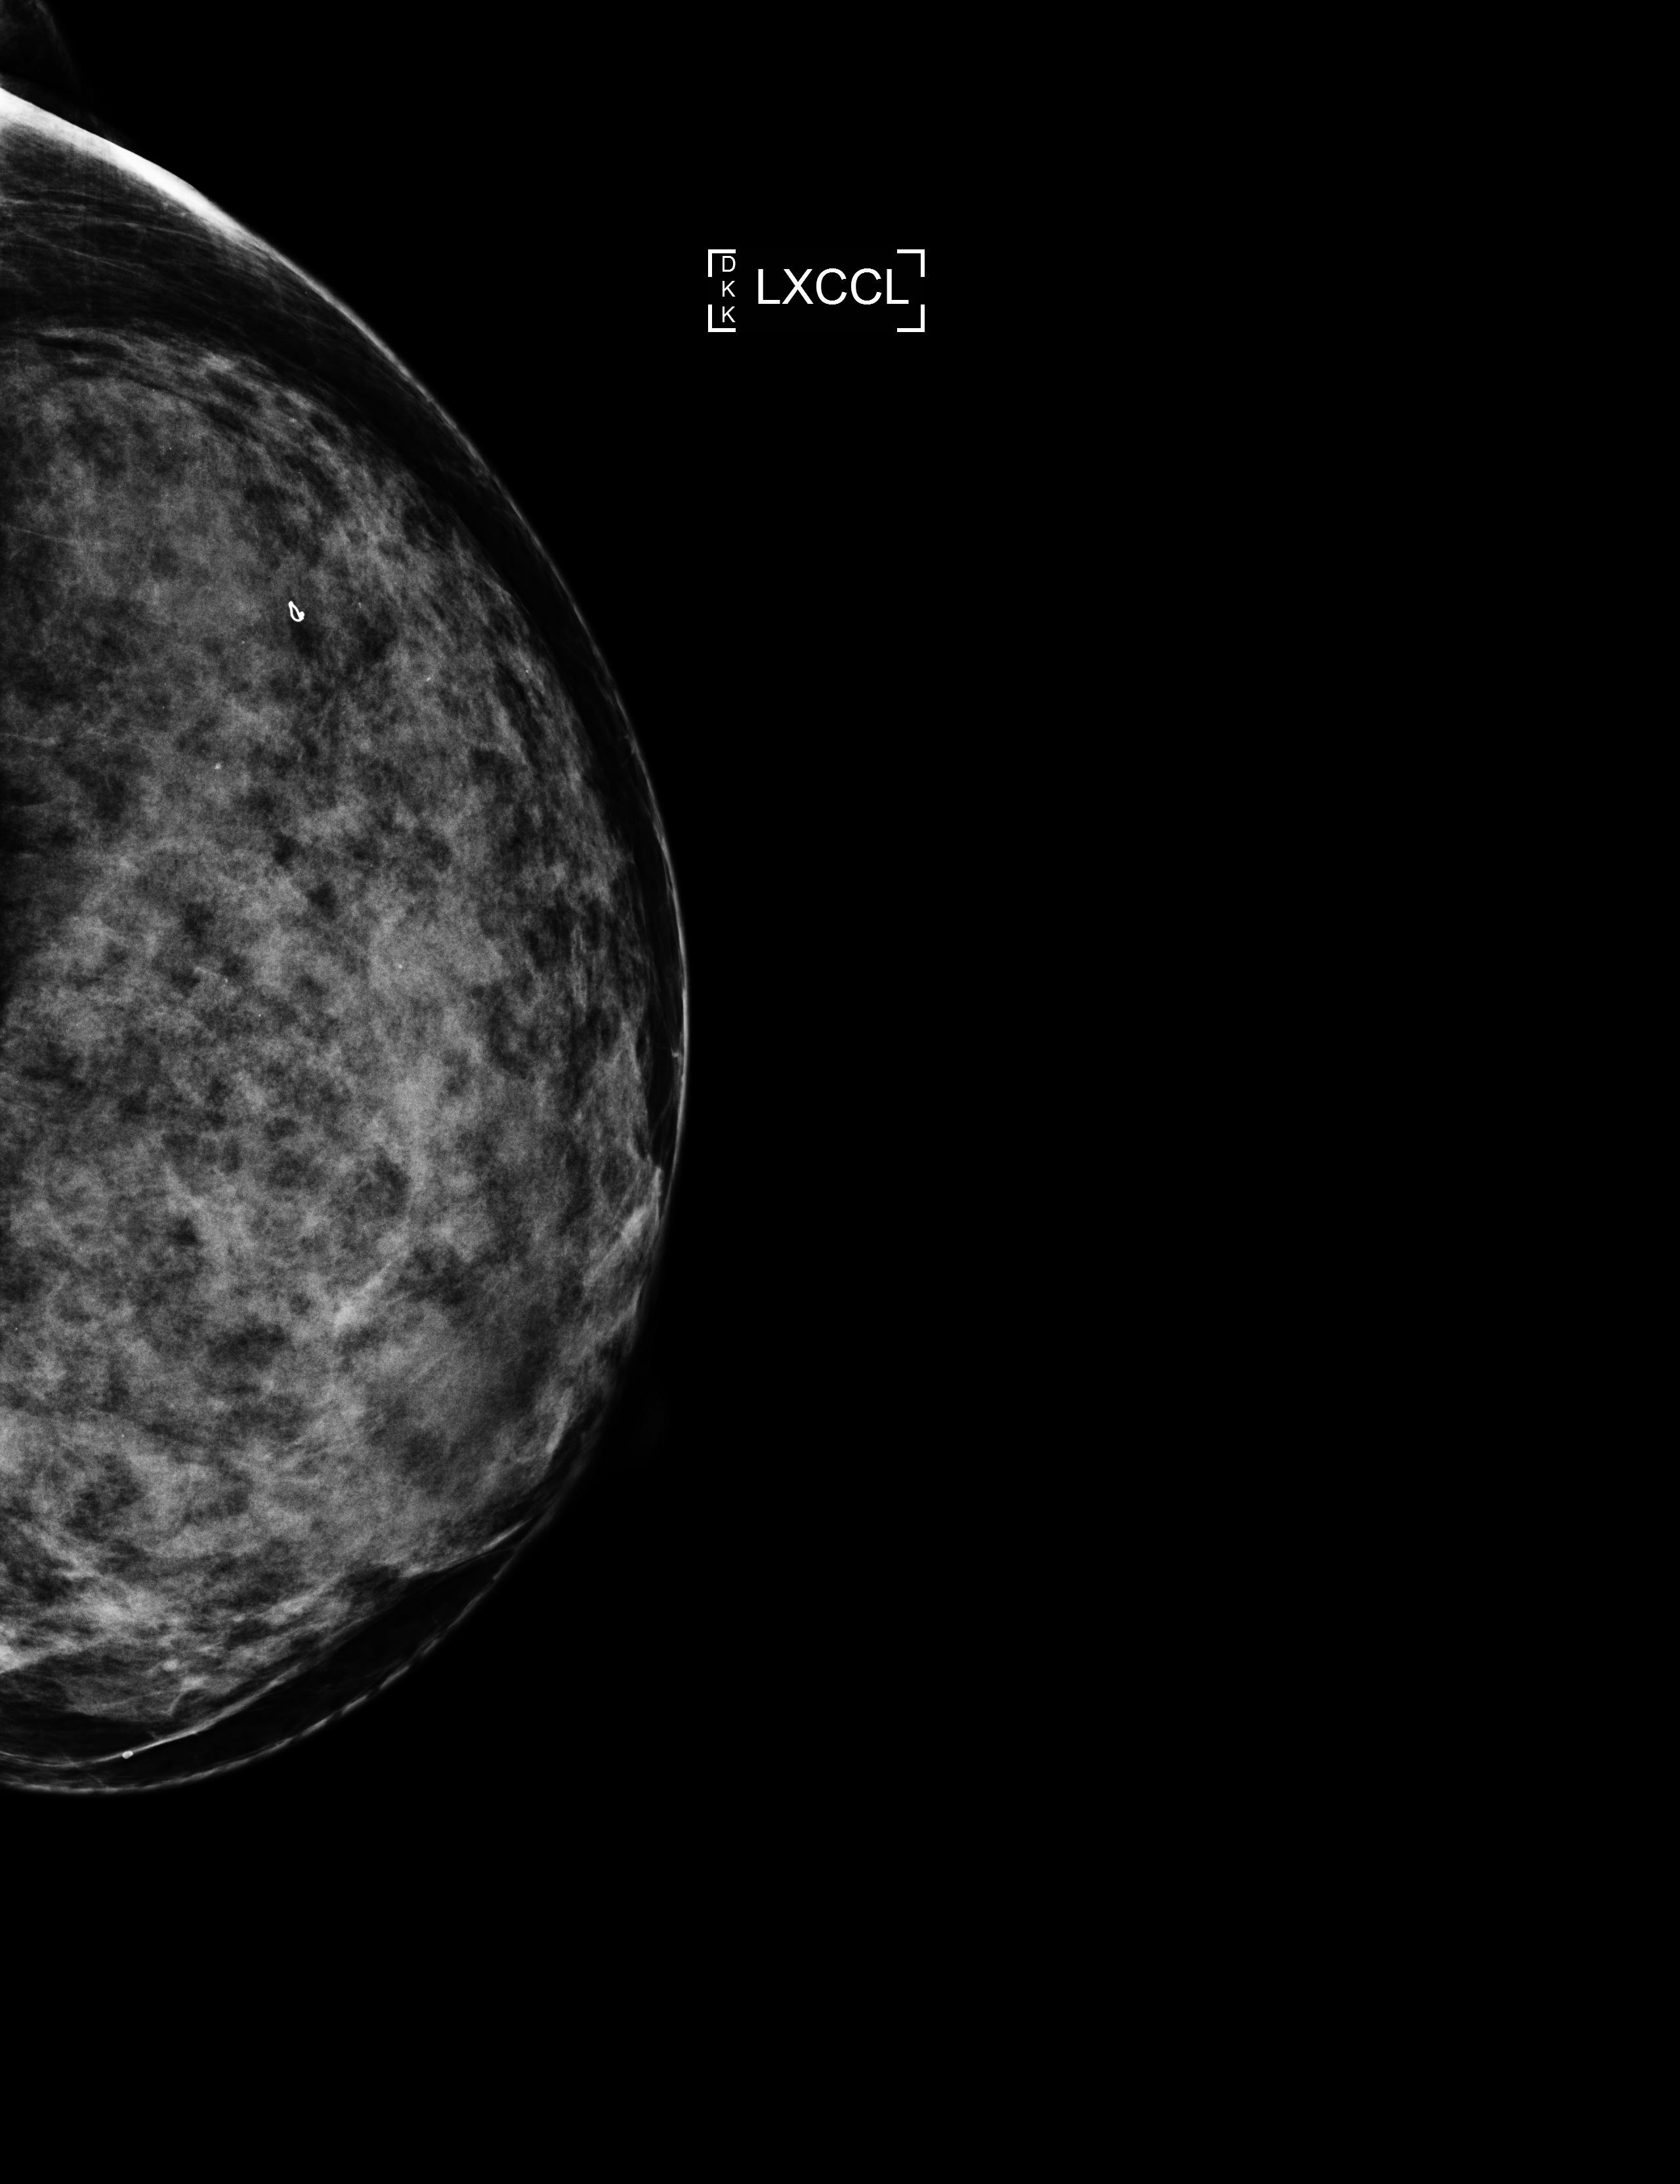
Screening examination, system: Selenia Dimensions. Patient: female, 63 years.
Image type: full-field digital mammogram. Breast: left. Projection: laterally exaggerated craniocaudal (XCCL) view.